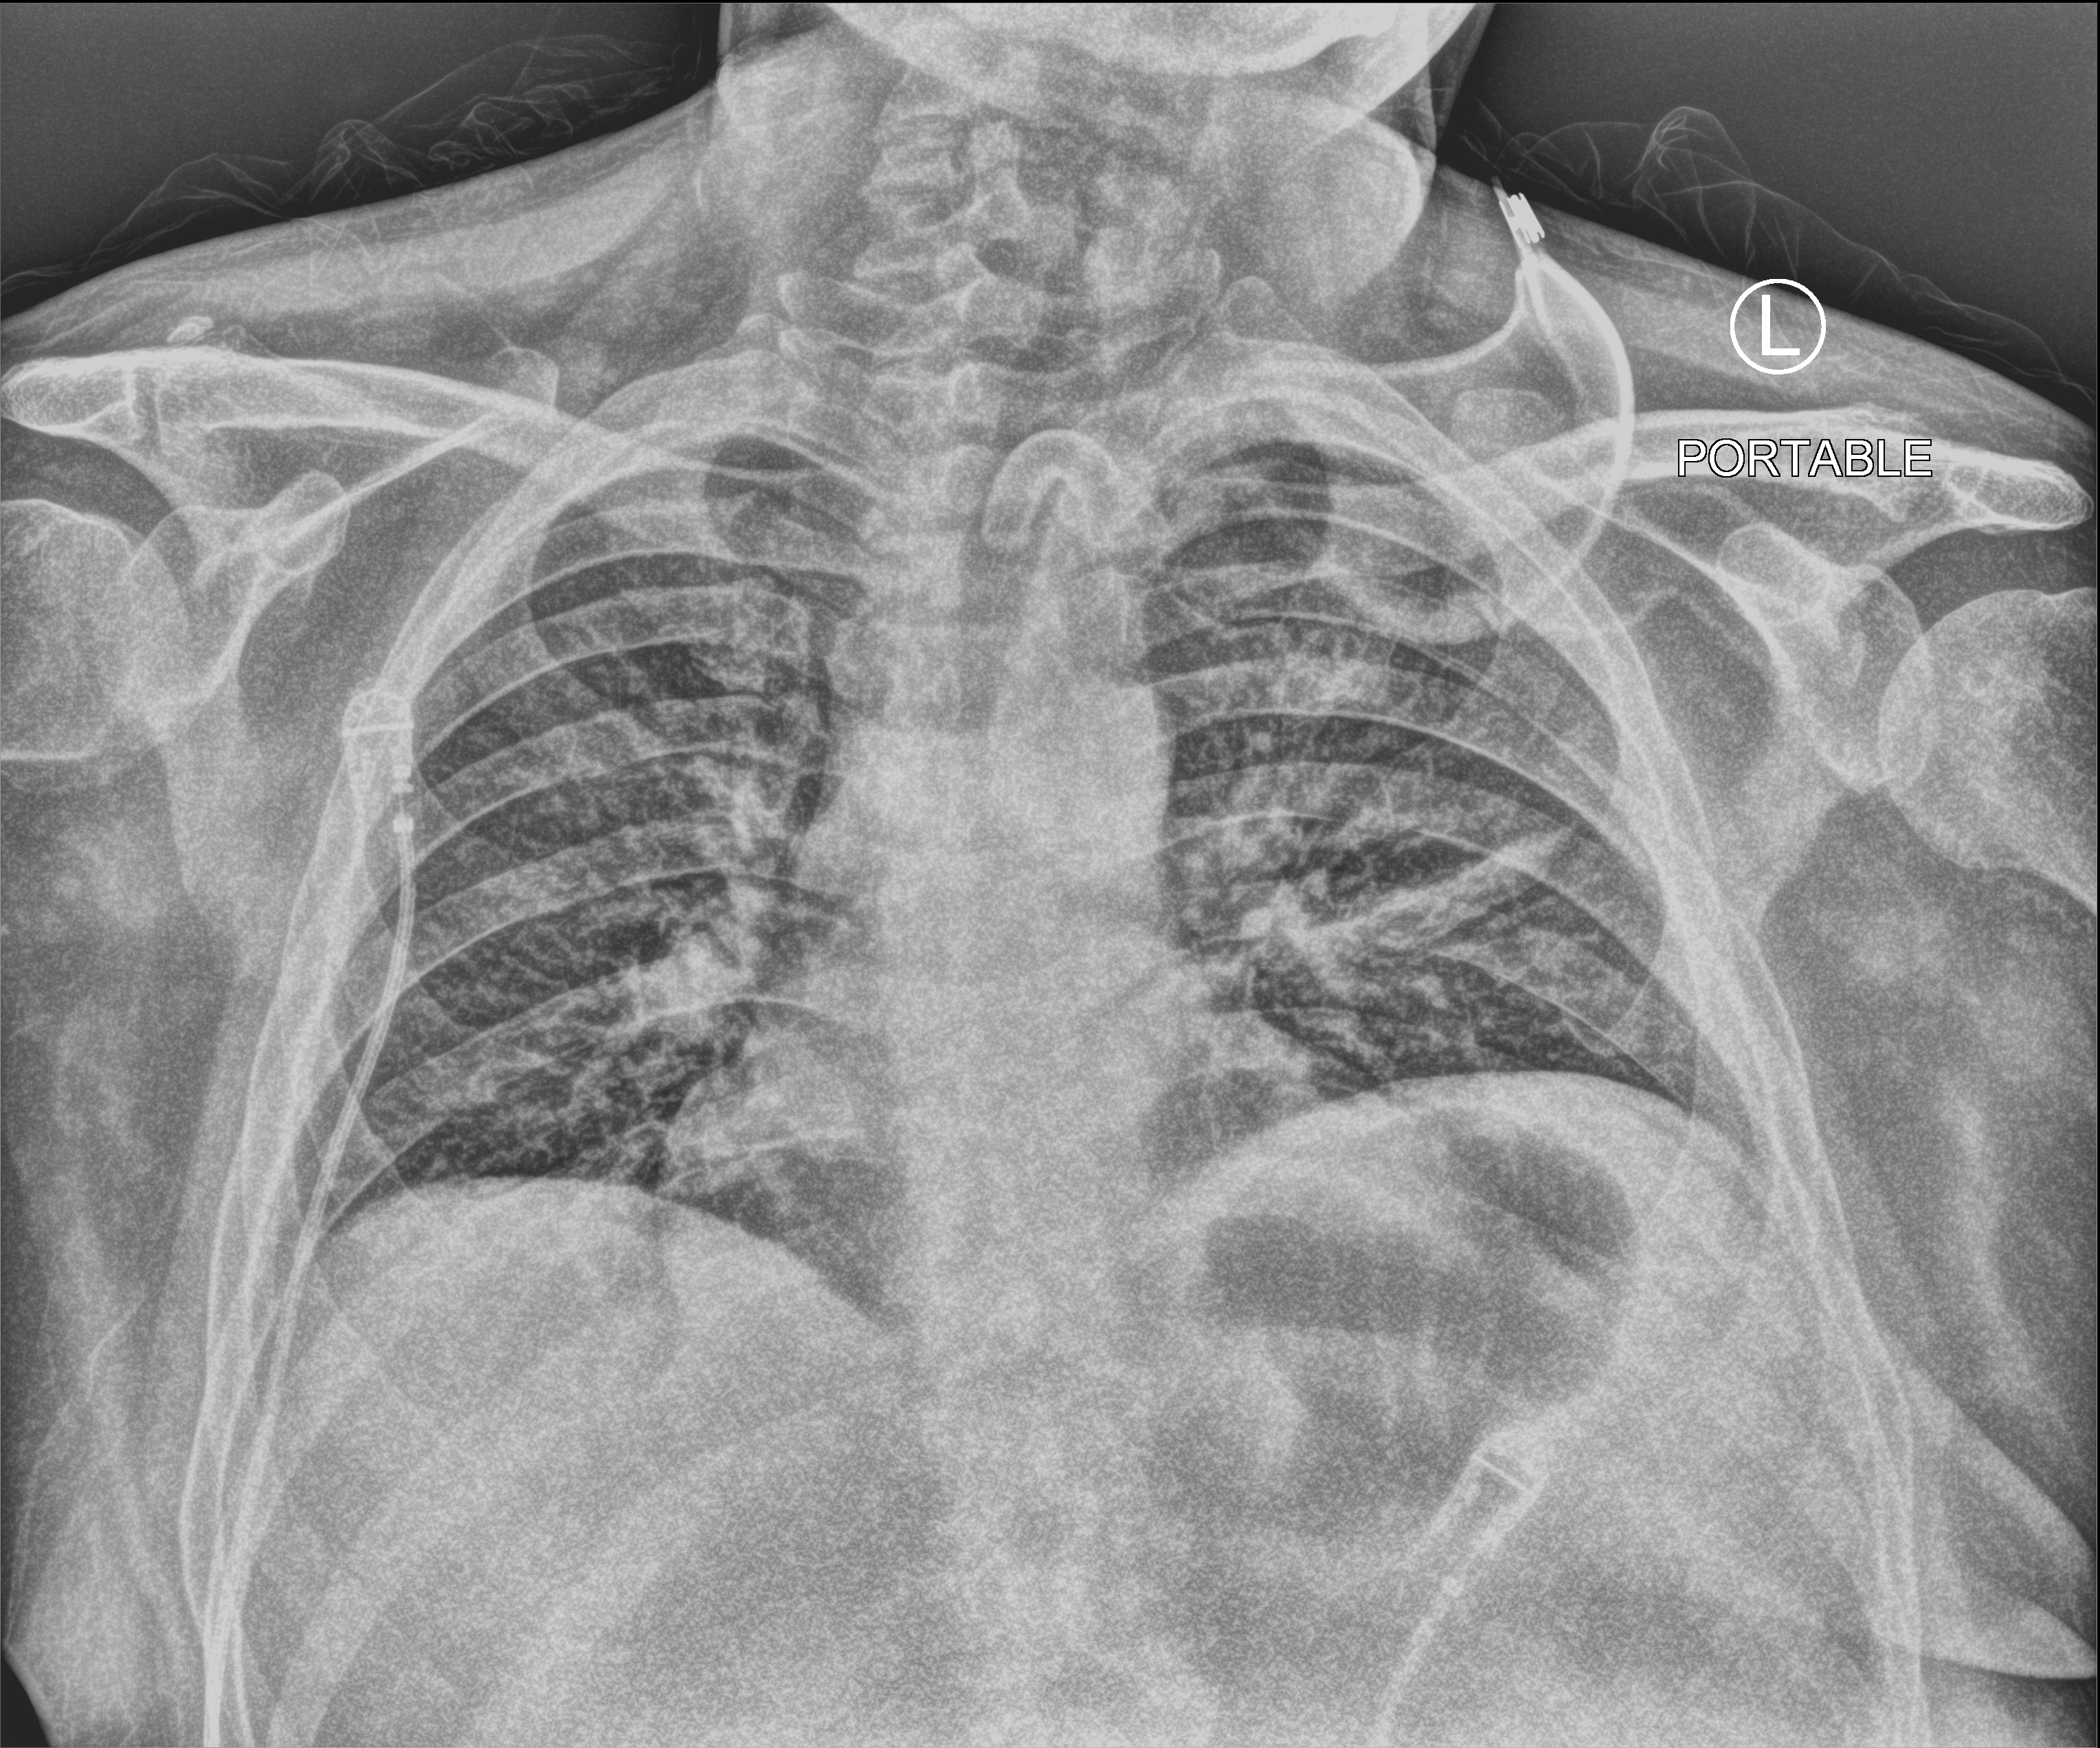
Portable chest radiograph, anteroposterior (AP) projection. Patient hospitalised with COVID-19; male, aged 18–59 years.
From the hospital-stay record, not from the radiograph (when in the stay this image was taken is not recorded):
- mechanically ventilated during this hospital stay: yes